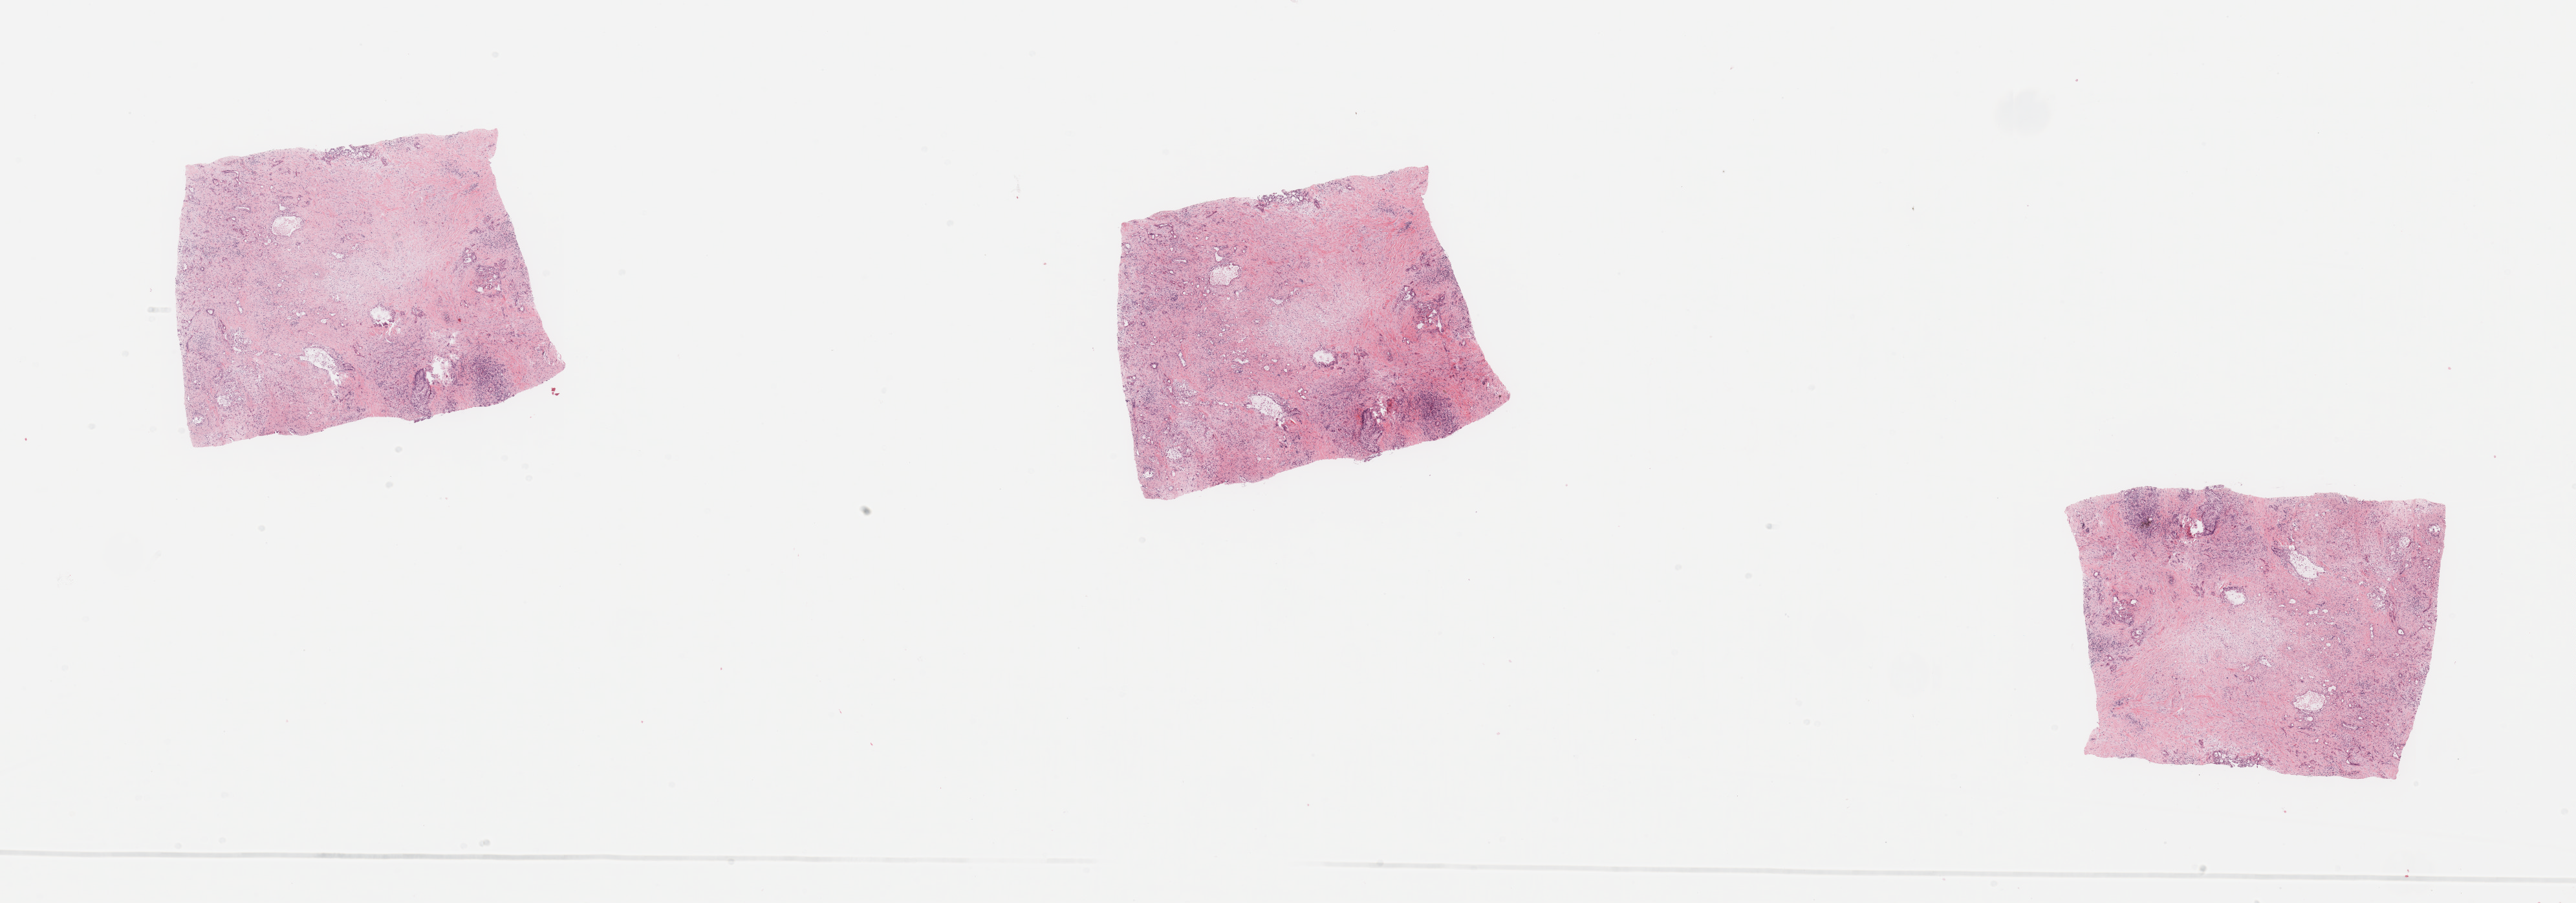
H&E-stained whole-slide image — low-resolution overview of the scanned area, about 31.5 x 11.0 mm, tumour tissue sample, sampled site: pancreas. 77-year-old male patient. Histologic grade: G2 (moderately differentiated). Slide review estimates, as recorded: tumour nuclei 20%, necrosis 0%.
Primary tumour site (as recorded): head. AJCC pathologic stage: III. Histologic diagnosis: Infiltrating duct carcinoma, NOS.